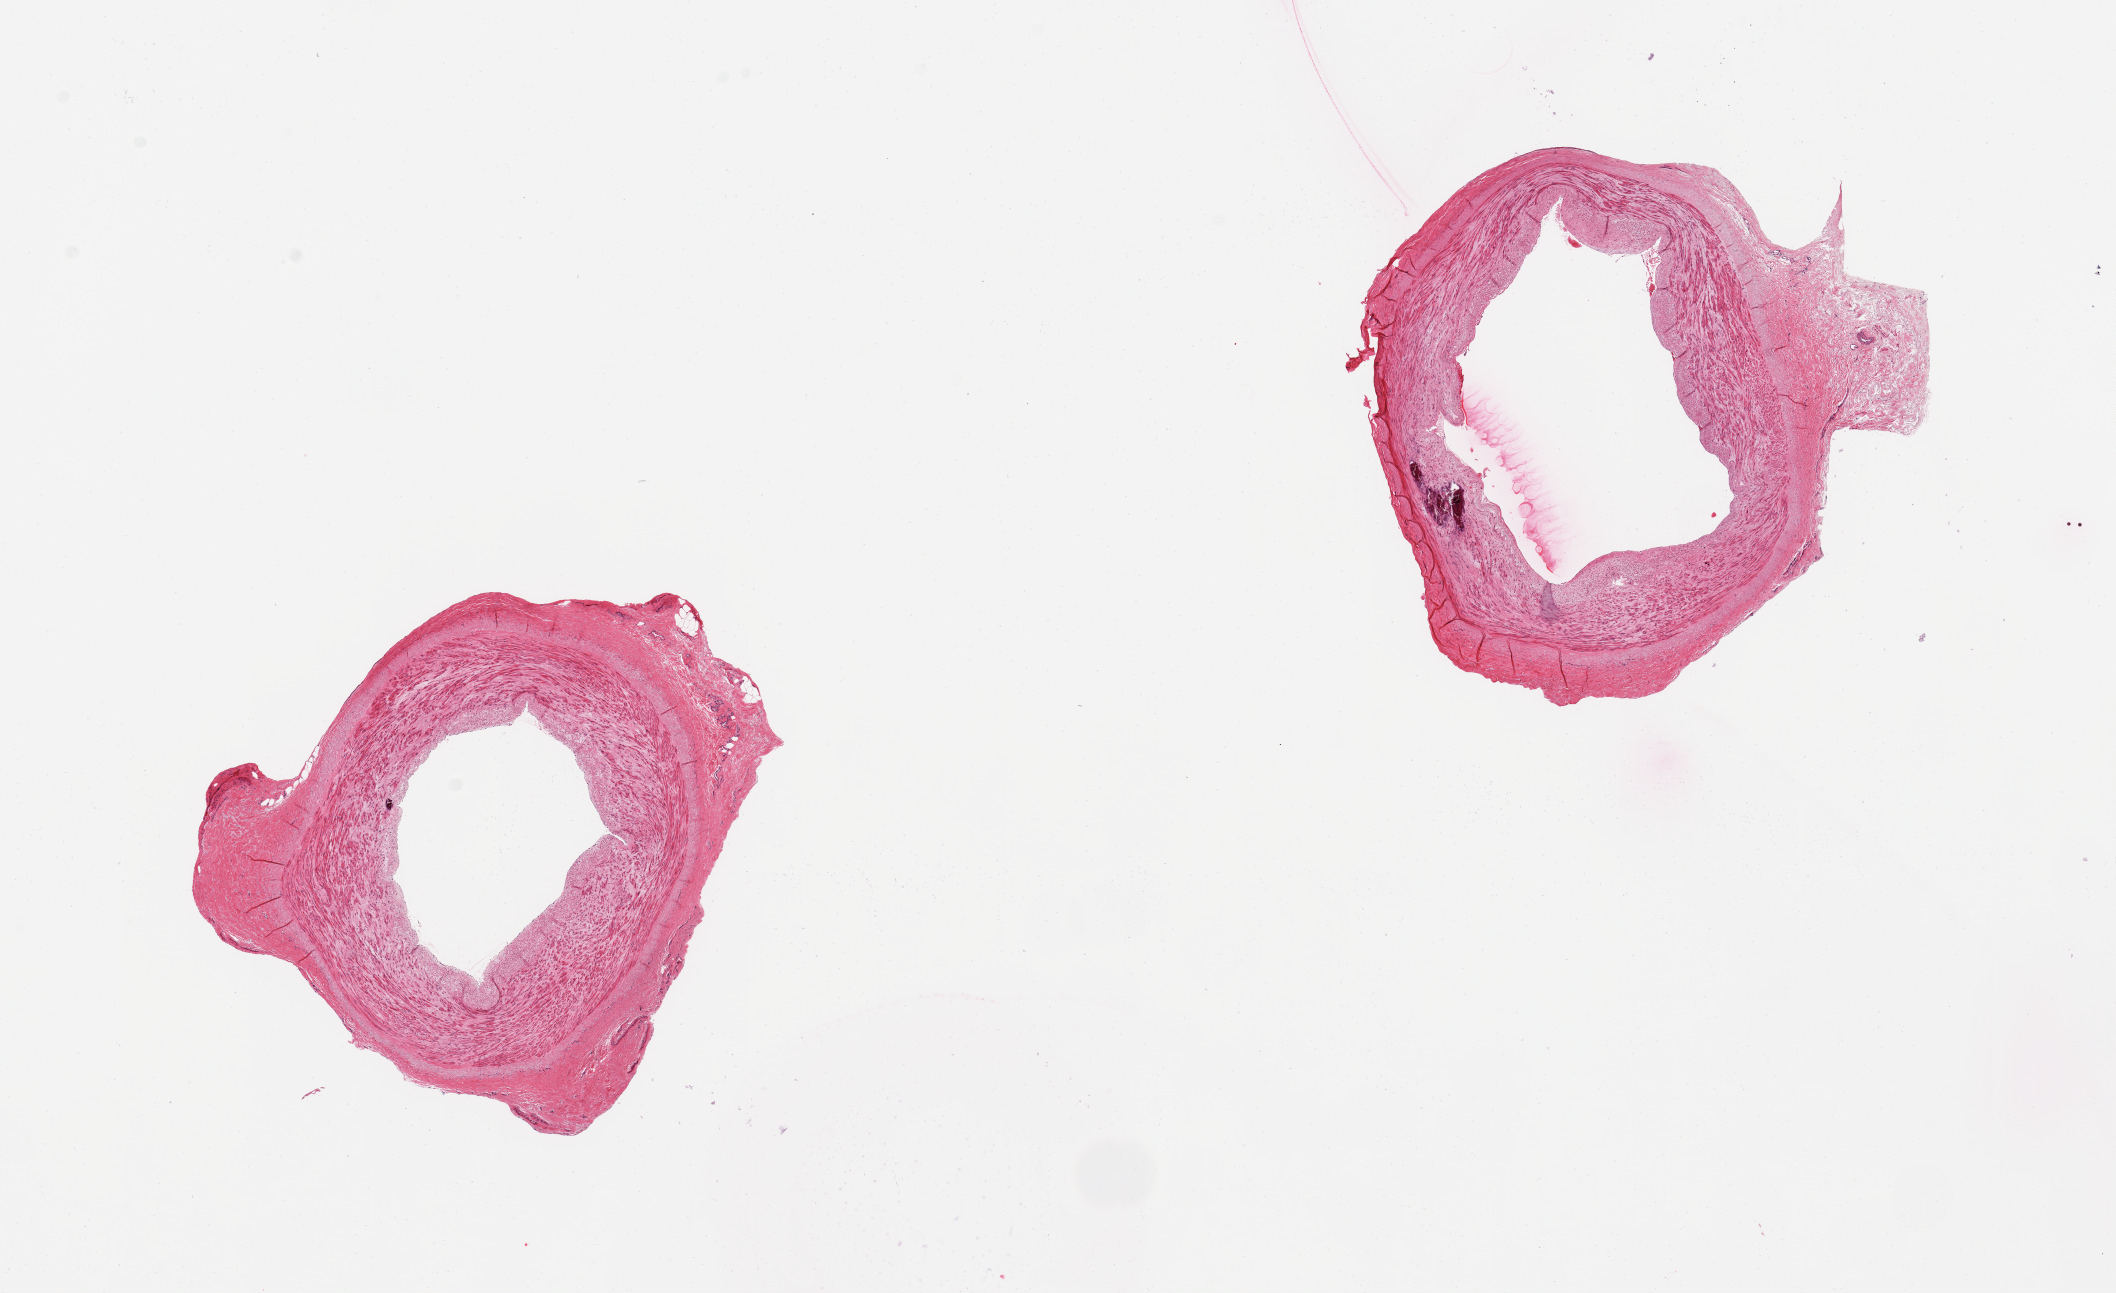
Whole-slide image, H&E stain, brightfield, whole scanned area (about 16.7 x 10.2 mm, from a 20x scan) shown as a low-resolution overview, PAXgene-fixed paraffin-embedded (PFPE) section, sampled site (target tissue): tibial artery, donor tissue sample. Donor sex: female.
Review note (as recorded): 2 pieces; mild plaque, focal medial calcification.